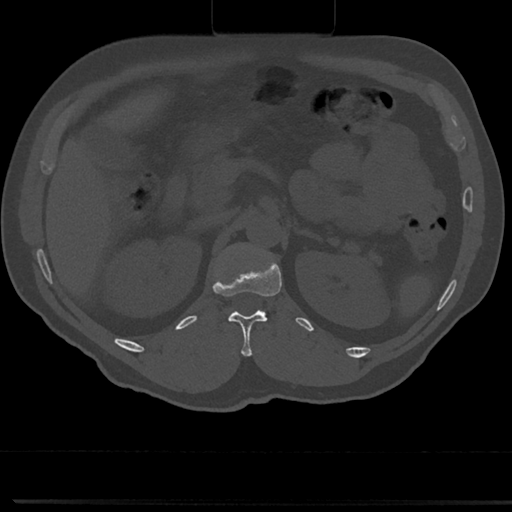
CT including the spine, one axial slice. Reconstruction kernel Br40s/3. 120 kVp. Bone window (W 1800 / L 400 HU). 512 × 512 image matrix, field of view 355 × 355 mm. Patient: male, 61 years. From the clinical record (not read from this slice): primary cancer: prostate.
Outlined on this slice (semi-automatically segmented with operator editing):
- L1 vertebra: bounding box [x1, y1, x2, y2] px = [212, 242, 270, 317]
- T12 vertebra: [226, 273, 282, 356]